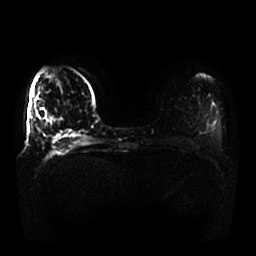
Breast MRI, one axial slice; position 7 of 25 along the scan axis; diffusion-weighted series; image 2 of 4 stored at this slice position (different b-values; order by instance number); 1.5 T; 256 × 256 image matrix, field of view 370 × 370 mm. Female patient.
Outlined on this slice (expert manual segmentation):
- tumour on diffusion-weighted imaging: bounding box <48,117,53,121> (left, top, right, bottom; pixels)